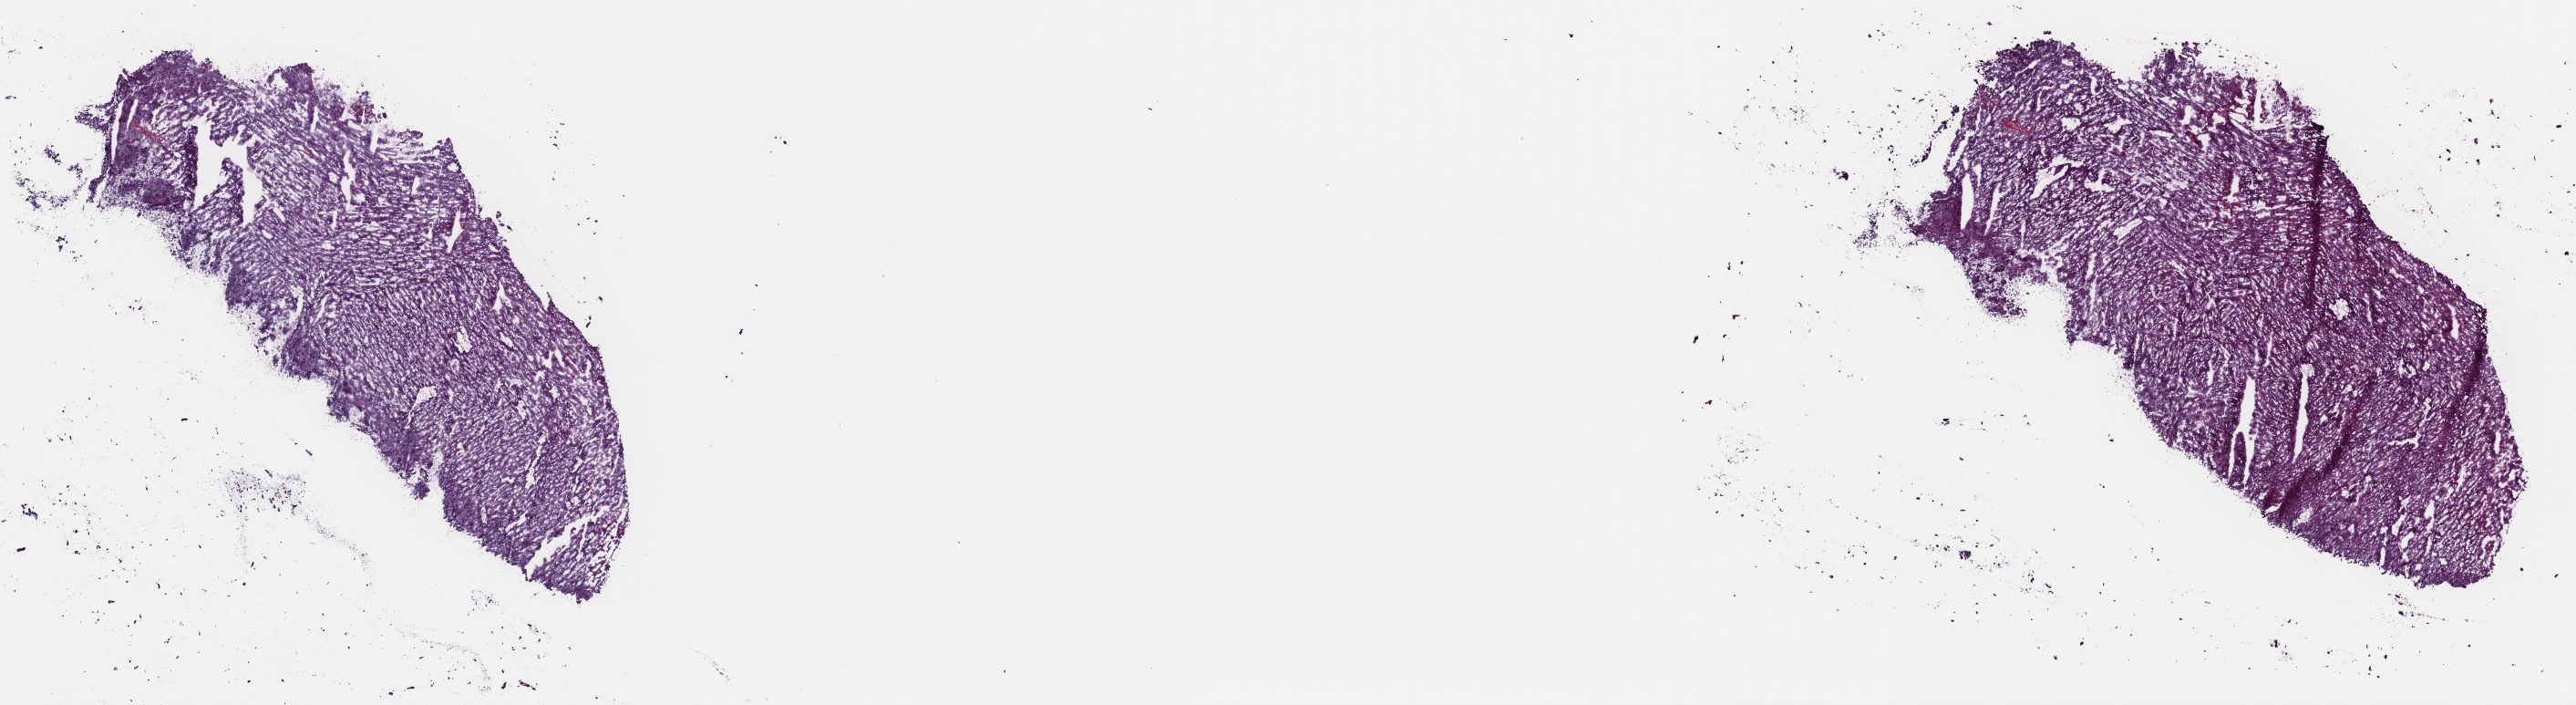
H&E-stained whole-slide image — whole scanned area (about 22.3 x 6.1 mm, acquisition: 40x scan) shown as a low-resolution overview; frozen section from the top of the tissue portion; adrenal cortex, primary tumour sample. Male, age 23 years at initial diagnosis. Pathologist review of this section (percent, as recorded): tumour cells 100%, tumour nuclei 85%, normal cells 0%, stromal cells 0%, necrosis 0%. Inflammatory infiltration, as recorded: lymphocyte infiltration 1%, monocyte infiltration 0%, neutrophil infiltration 0%.
Lymph nodes positive (case pathology): 0 of 32 examined. Diagnosis: Adrenal cortical carcinoma (cortex of adrenal gland).